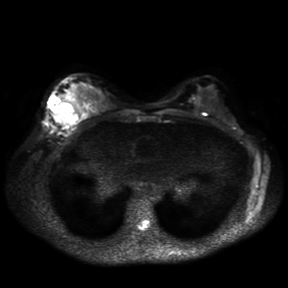
Breast MRI, one axial slice; position 19 of 30 along the scan axis; diffusion-weighted series; image 2 of 4 stored at this slice position (different b-values; order by instance number); 3 T; 4 mm slice thickness; 288 × 288 image matrix, field of view 360 × 360 mm. Female patient.
Annotated regions visible in this slice (expert manual segmentation):
- tumour on diffusion-weighted imaging: bounding box <50,103,61,123> (left, top, right, bottom; pixels)